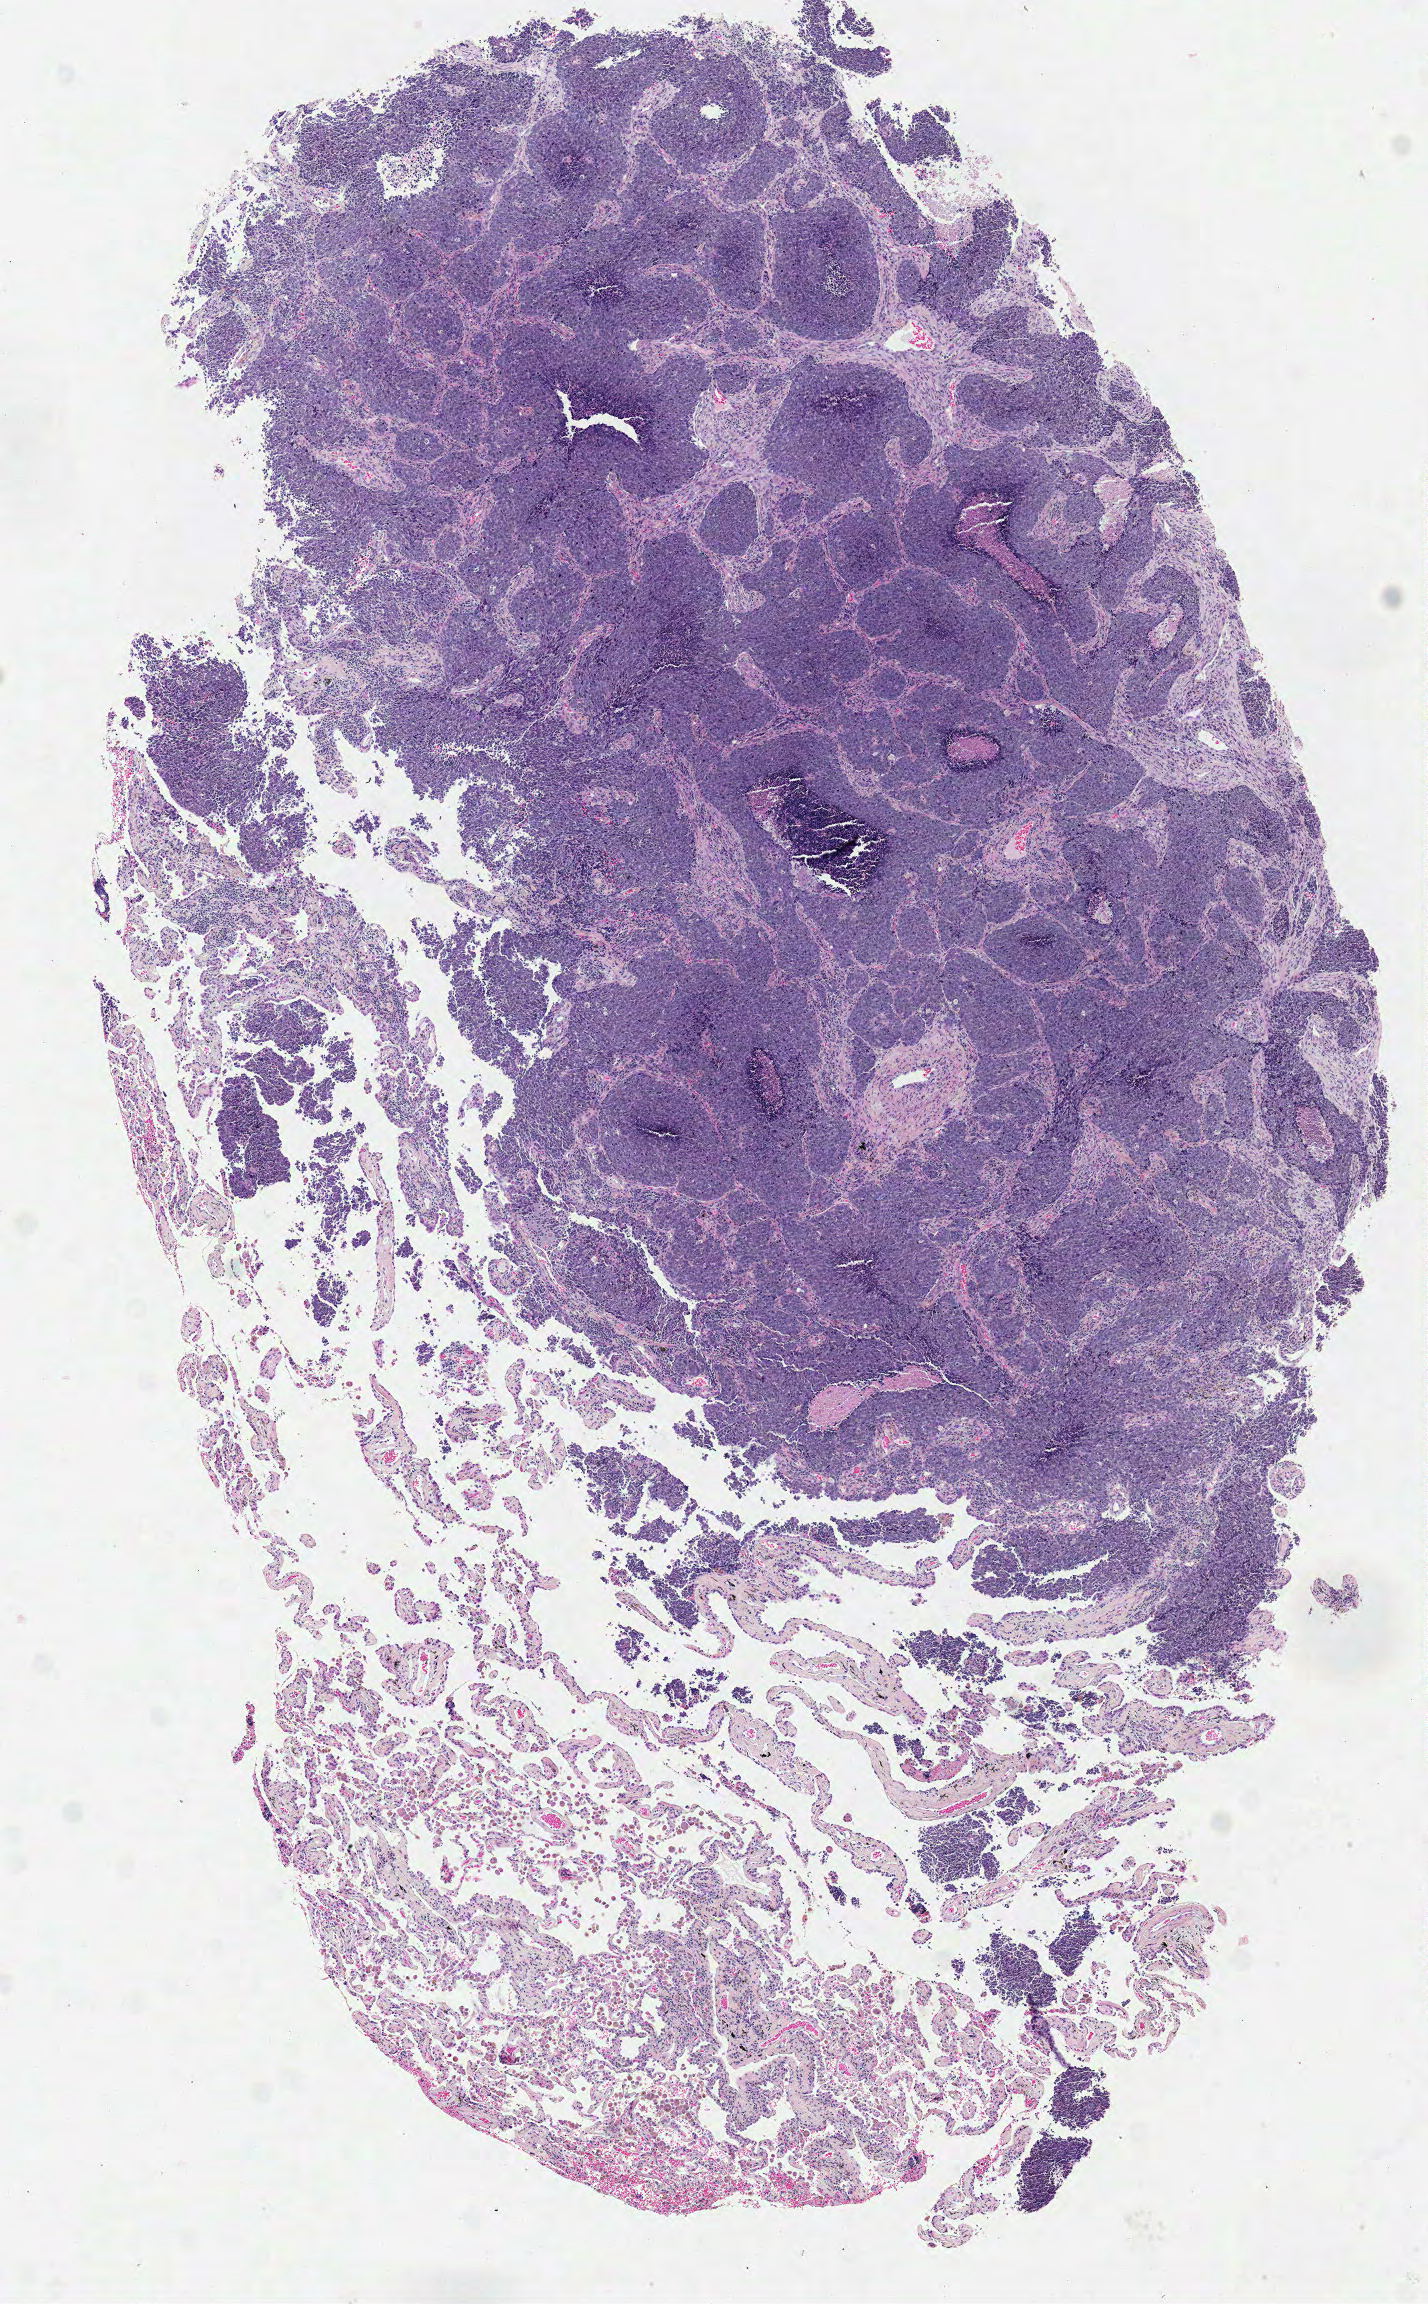
Whole-slide histology image, Hematoxylin and eosin (H&E) stained — a low-resolution overview of the entire scanned area, about 5.6 x 9.1 mm. Formalin-fixed paraffin-embedded (FFPE) diagnostic section. Lung, primary tumour sample. Patient: female, age at initial diagnosis 65 years.
AJCC pathologic stage: IA (6th edition). Pathologic diagnosis: Squamous cell carcinoma, NOS.